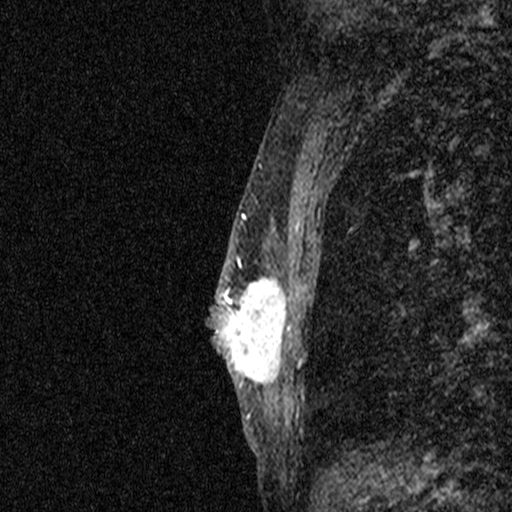
Breast MRI (dynamic contrast-enhanced), one sagittal slice; slice 25 of 44 in the series (ordered by position); dynamic contrast-enhanced study with each time point stored as its own series, time point 2 of 3 at this slice position (early post-contrast, ordered by acquisition time); 1.5 T; TE 4.5 ms, TR 11 ms; 2.05 mm slice thickness; 512 × 512 image matrix. Female patient, age 44 years. Case-level facts recorded for this patient, not image findings: setting: breast cancer imaged before/during neoadjuvant chemotherapy; receptor status: HR-positive, HER2-negative.
Outlined on this slice (semi-automatic segmentation, software-assisted and operator-edited):
- analysis volume of interest (the breast-tissue region the enhancement analysis was run in; not a lesion): bounding box (x1, y1, x2, y2) in pixels: (204, 254, 284, 401)
- tumour enhancement mask (voxels above the 90 % enhancement threshold inside the analysis volume of interest): (211, 257, 284, 388)